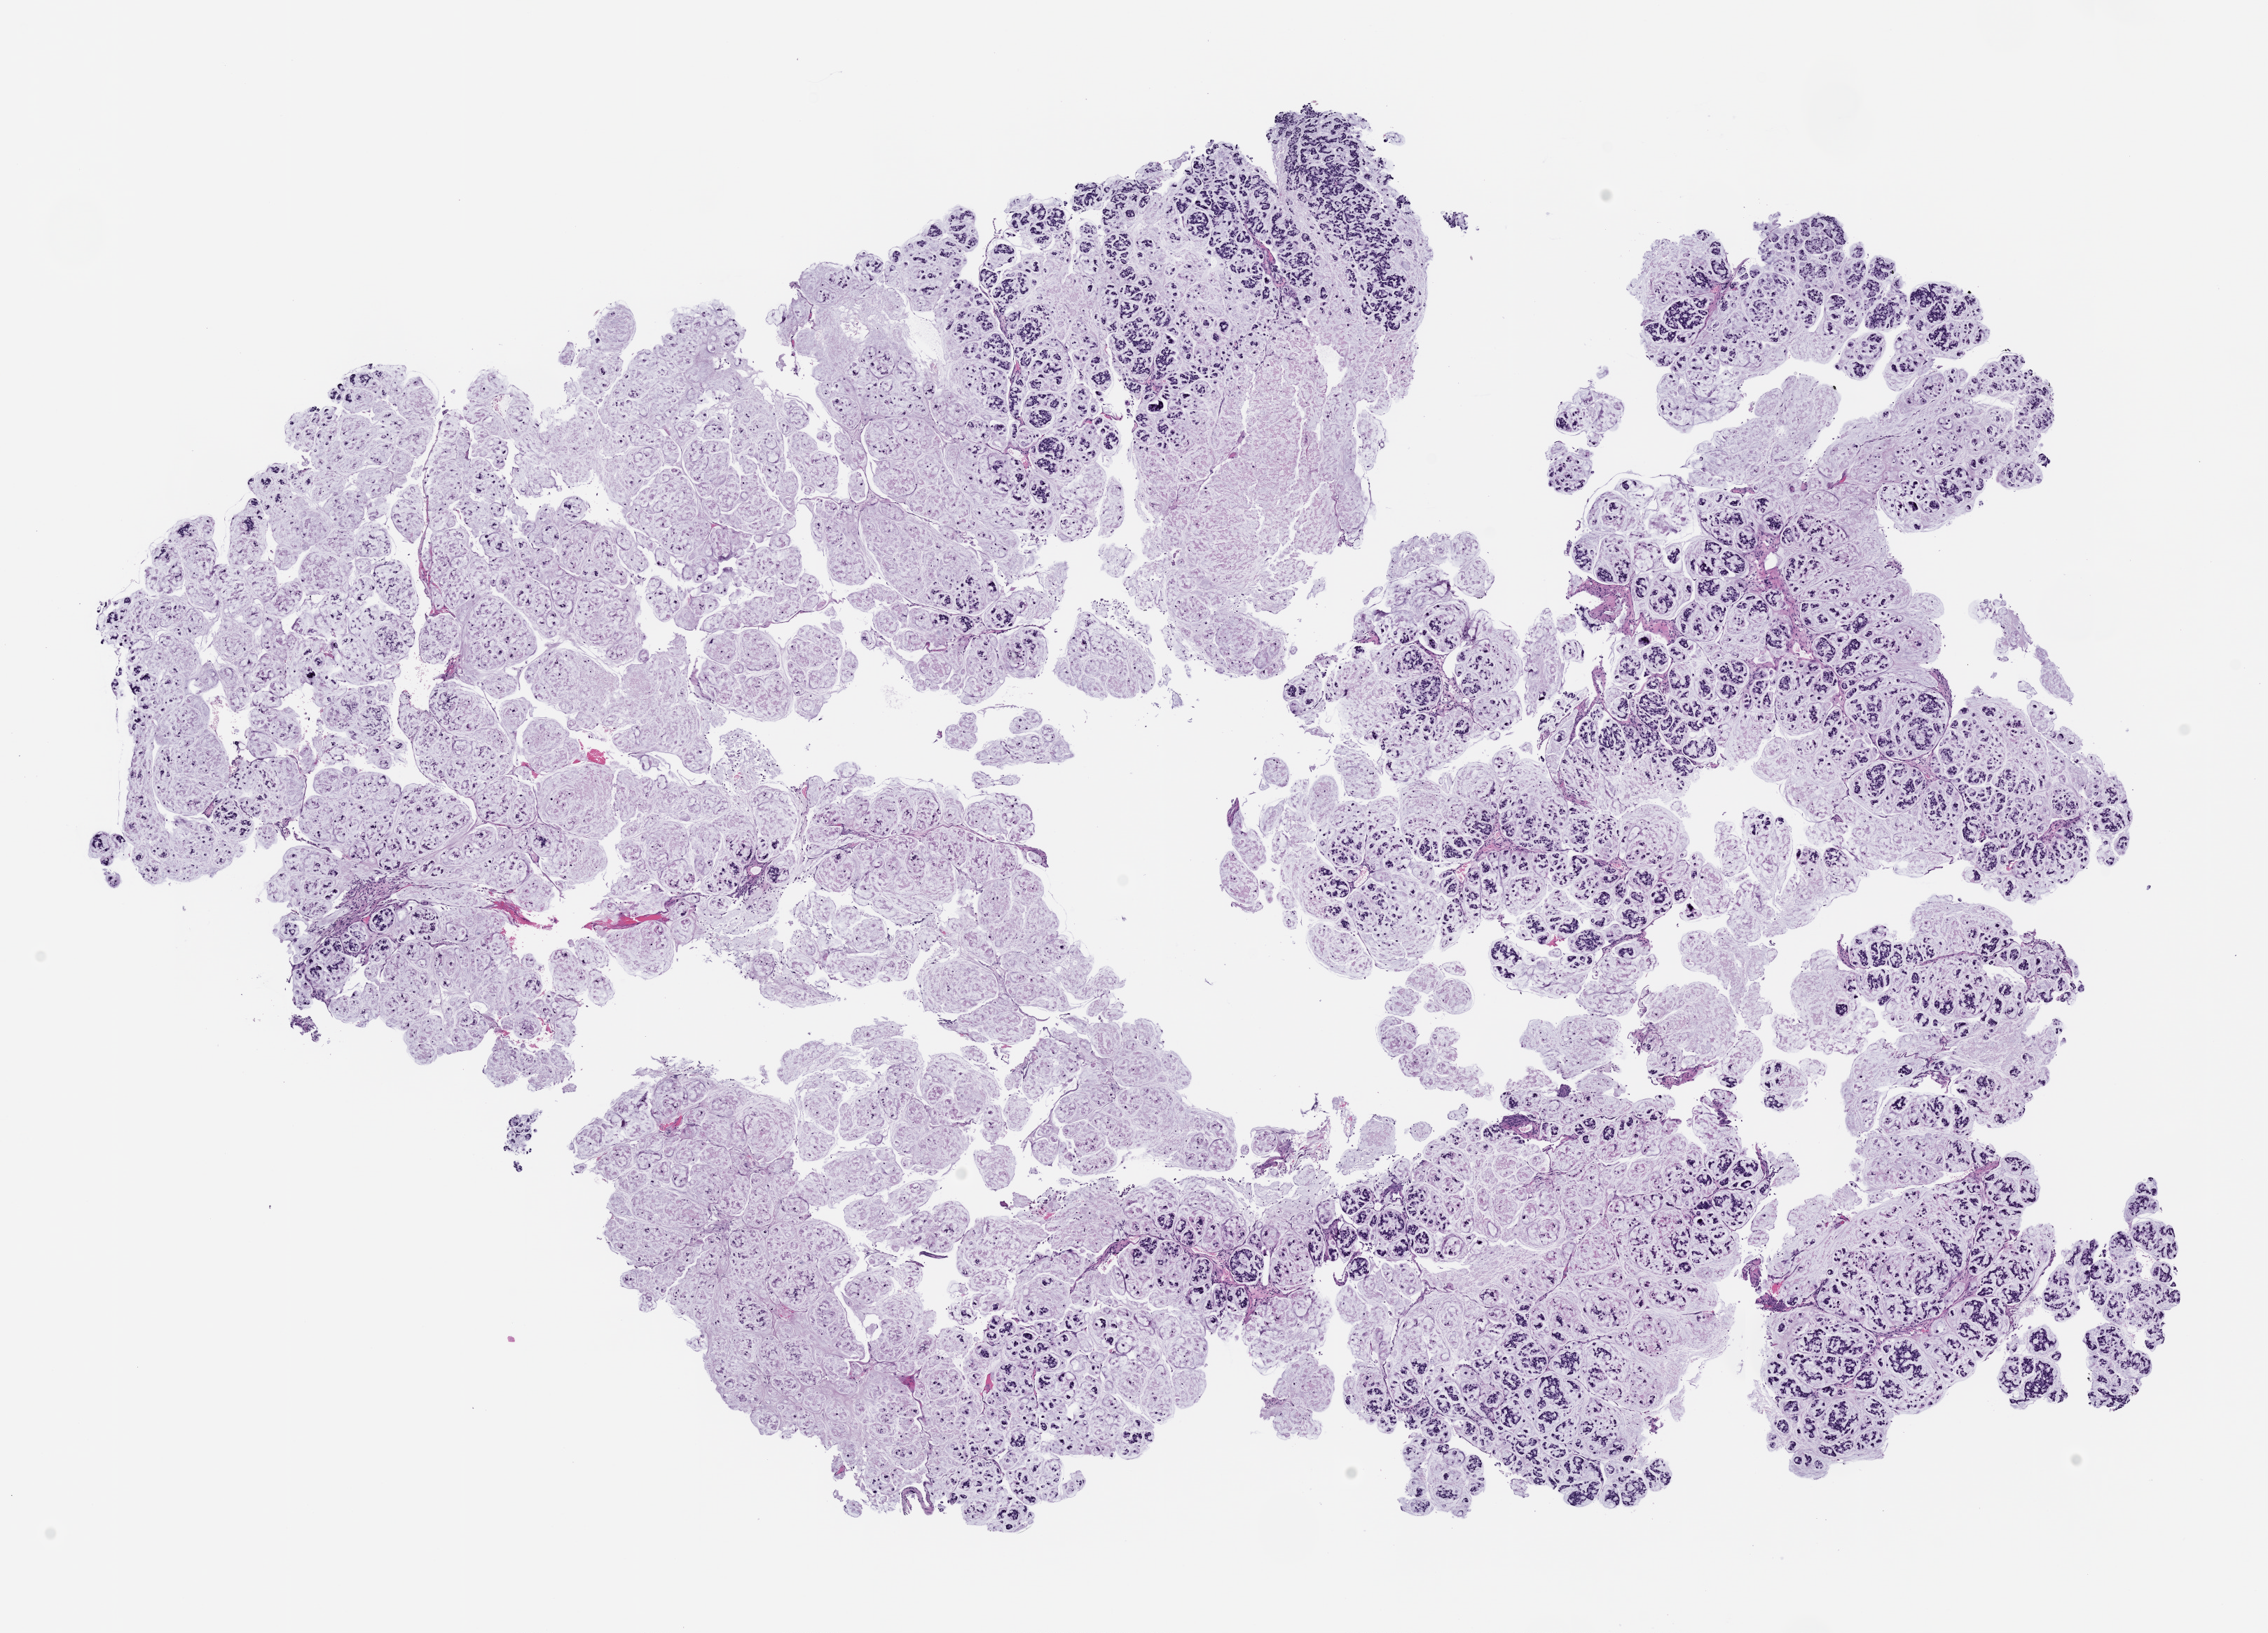
Whole-slide image, H&E: patient-derived xenograft (human tumor grown in a mouse), passage 2, a low-resolution overview of the entire scanned area, about 13.0 x 9.4 mm; formalin-fixed paraffin-embedded section; tumor site category: colon.
Originating patient diagnosis: Colon Adenocarcinoma.